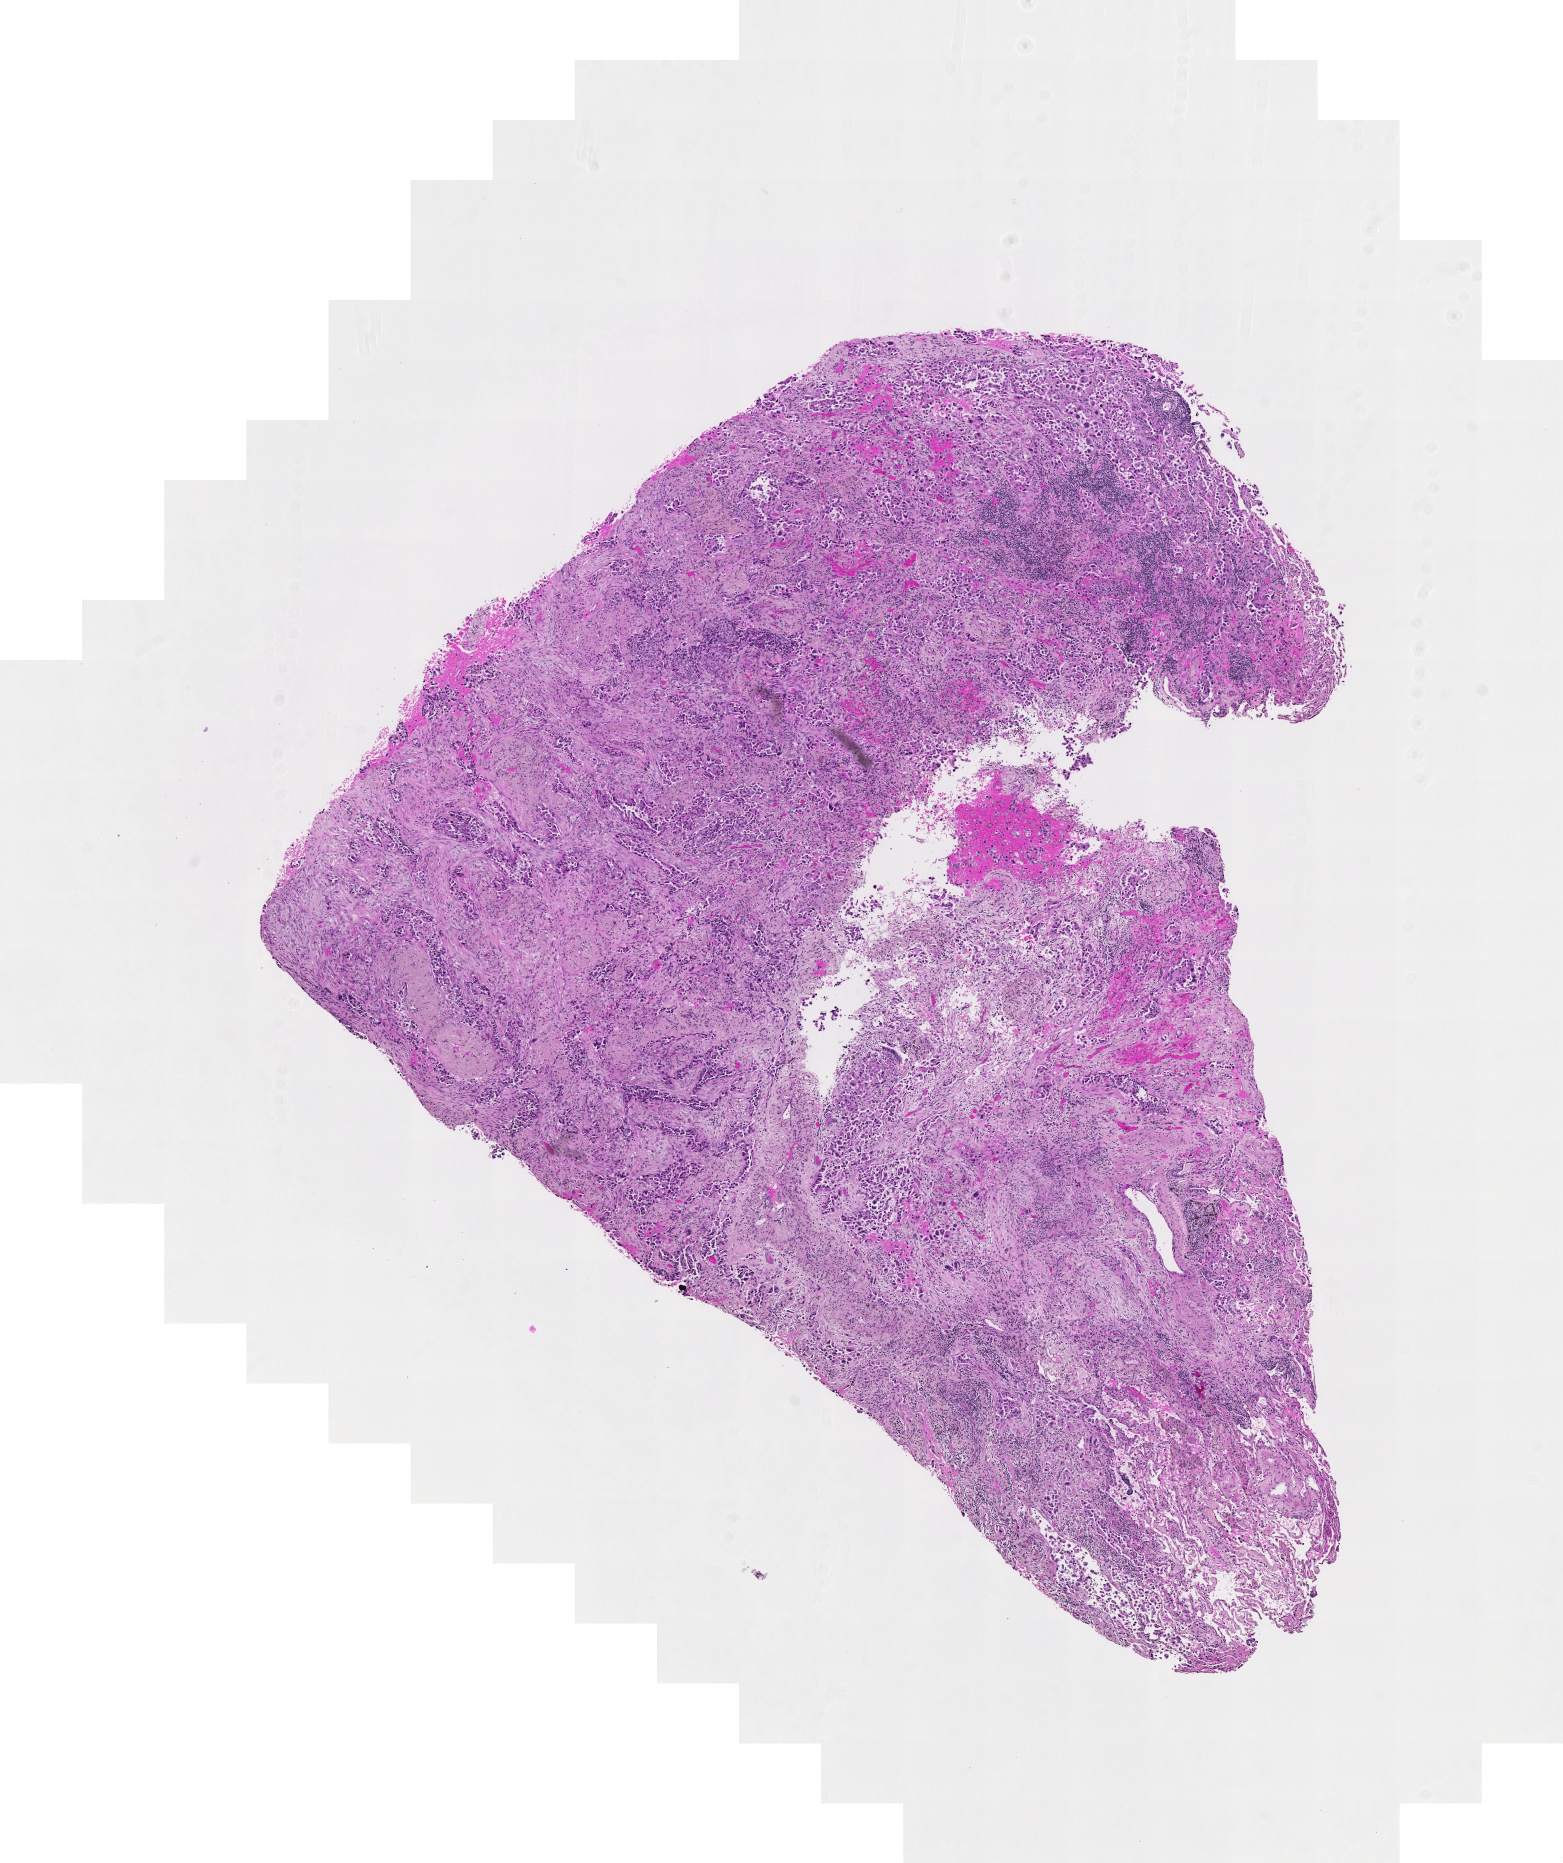
Whole-slide histology image, Hematoxylin and eosin (H&E) stained — a low-resolution overview of the entire scanned area, about 8.1 x 9.6 mm, lung, tumour tissue. Female, 68 y/o. Histologic grade: G2 (moderately differentiated).
Histologic diagnosis: Adenocarcinoma, NOS. AJCC pathologic stage: IIIA.